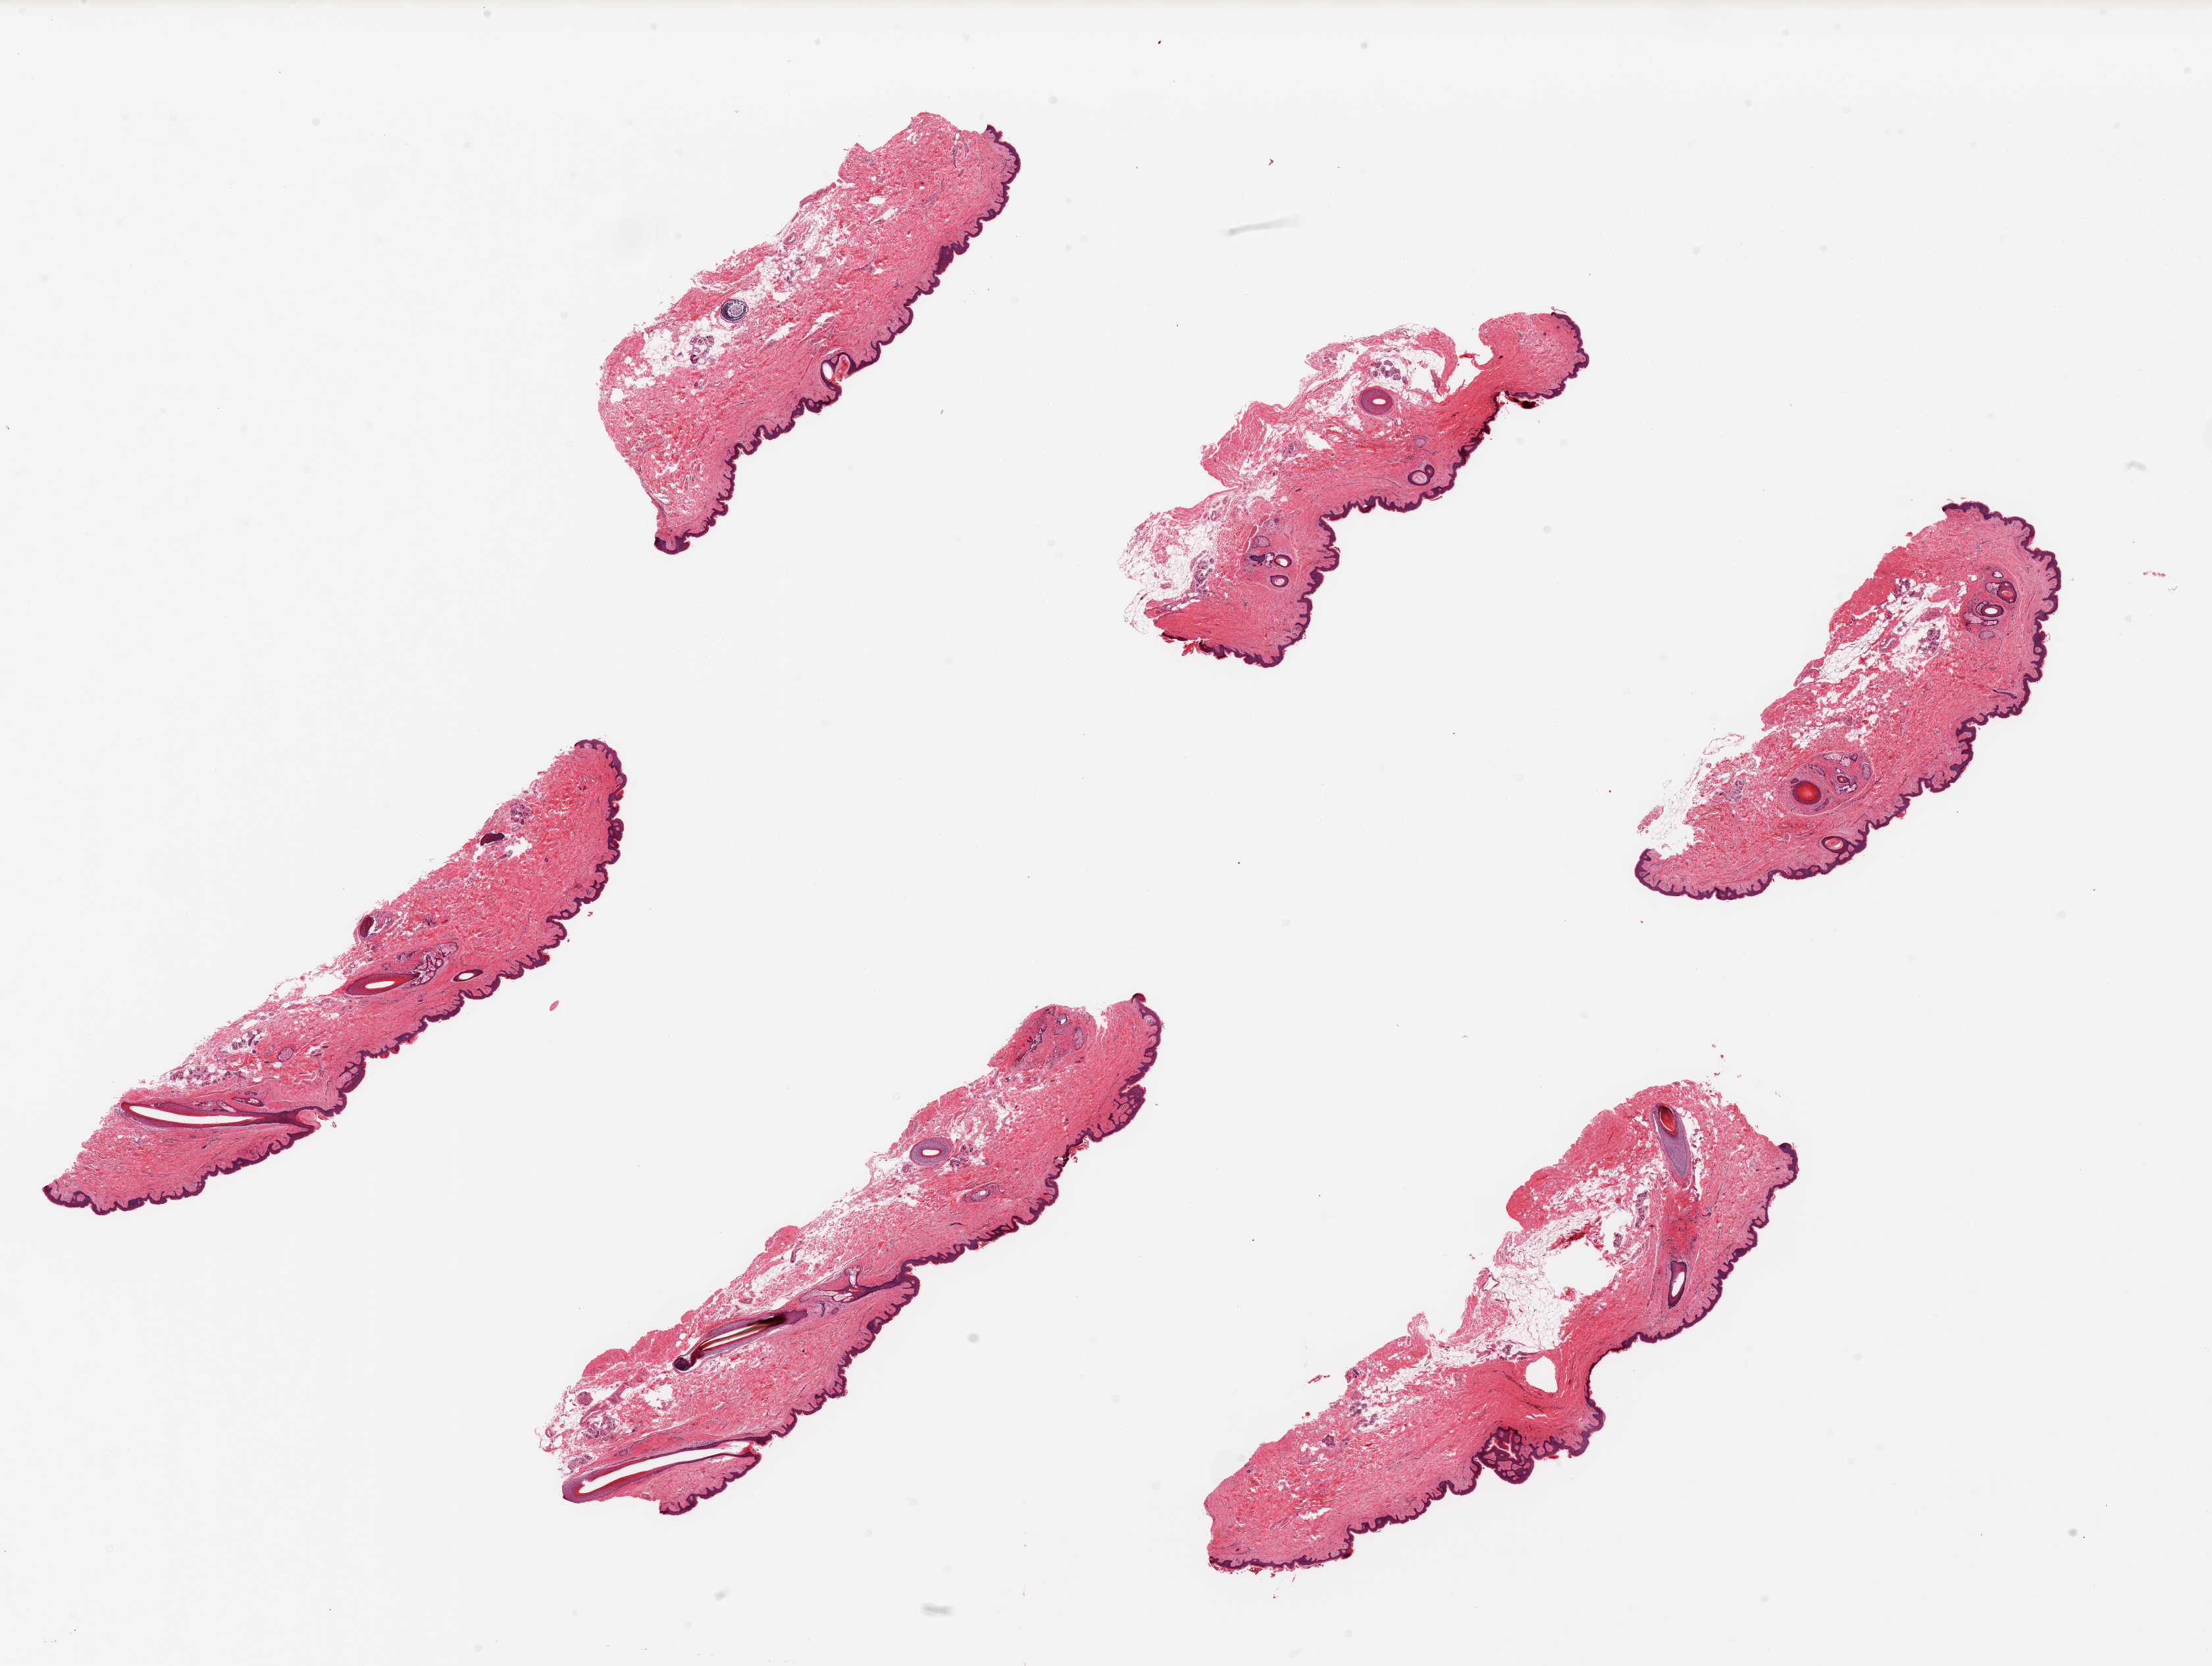
Whole-slide image, haematoxylin and eosin stain, brightfield, a low-resolution overview of the entire scanned area, about 26.6 x 20.0 mm (acquisition: 20x scan). PAXgene-fixed paraffin-embedded (PFPE) section. Section of skin of suprapubic region (target tissue). Tissue donor sample. Donor sex: female.
Pathologist's review note for this sample: 6 pieces; hair bearing skin with ~20% external/internal fat.